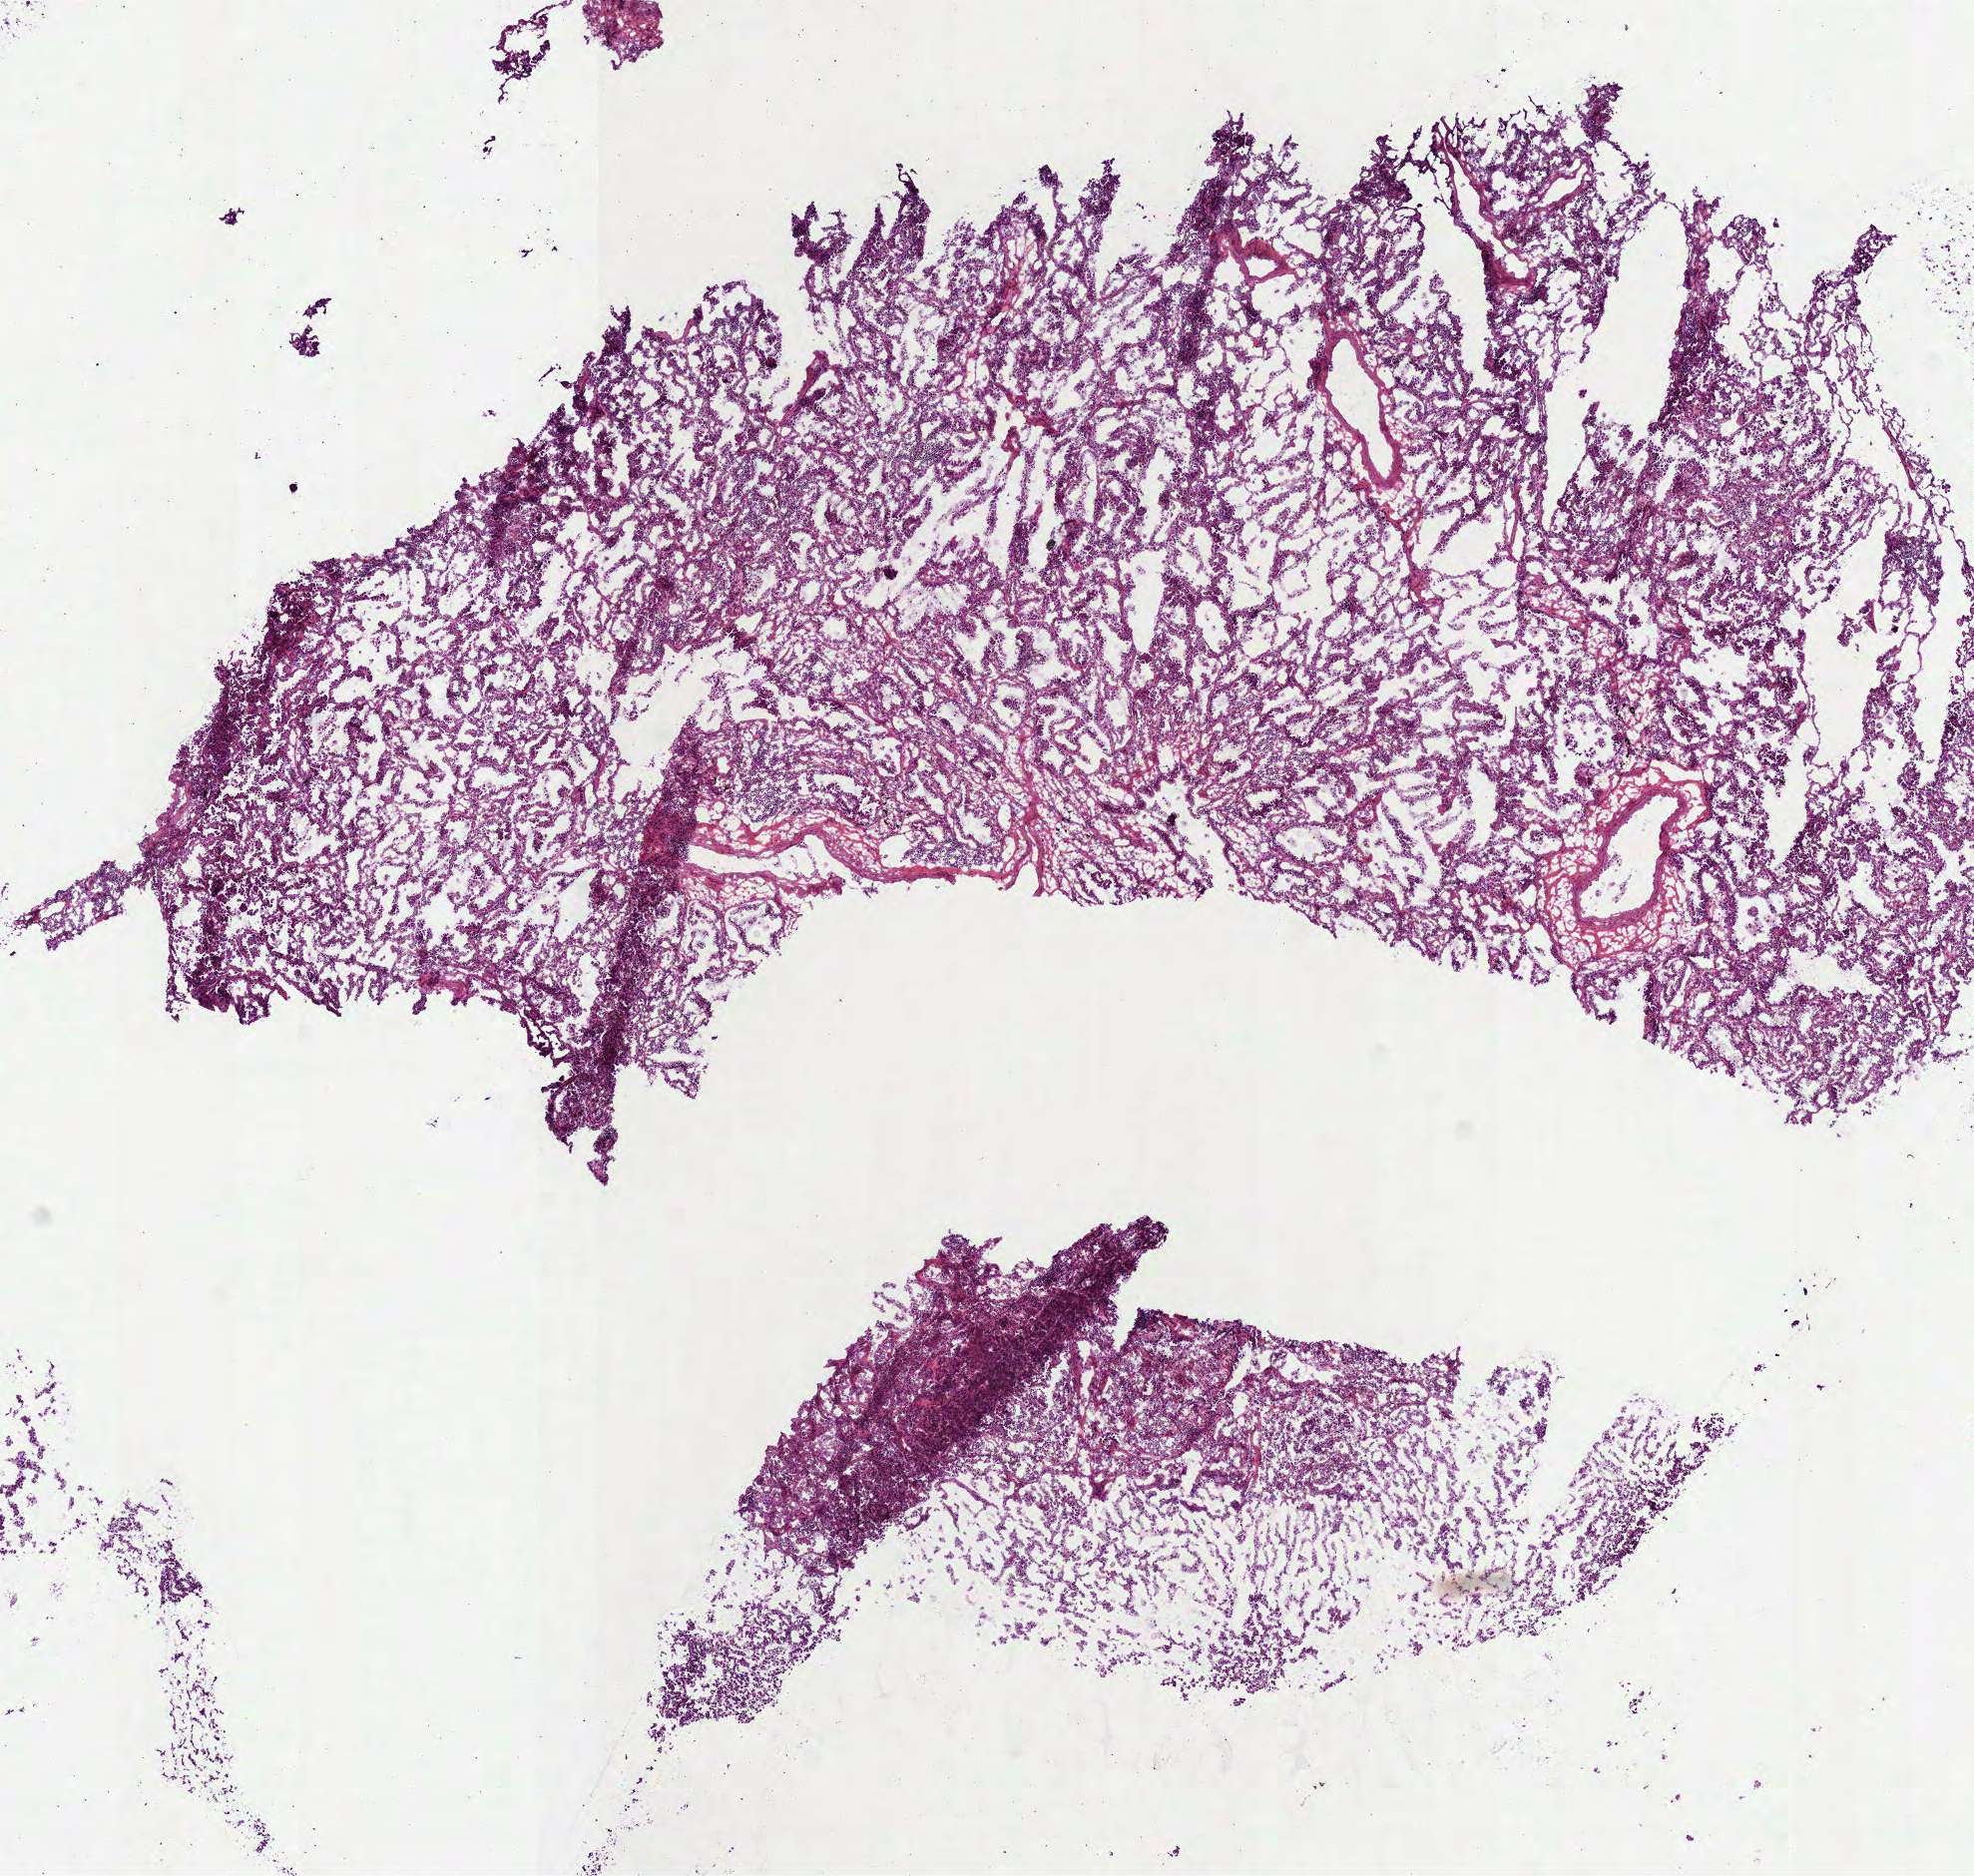
Whole-slide histology image, Hematoxylin and eosin (H&E) stained — whole scanned area (about 8.0 x 7.6 mm) shown as a low-resolution overview; frozen section; lung, primary tumour sample. Patient: male, age at initial diagnosis 74 years. Pathologist review of this section (percent, as recorded): tumour cells 85%, tumour nuclei 80%, normal cells 0%, stromal cells 15%, necrosis 0%.
* diagnosis: Papillary adenocarcinoma, NOS (upper lobe, lung)
* TNM: T1a N0 M0
* AJCC pathologic stage: IA